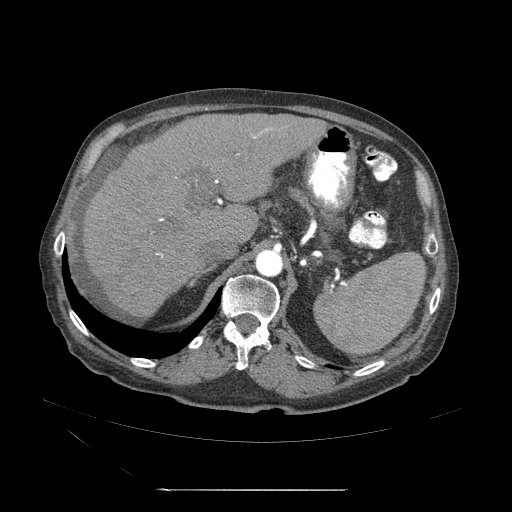
Contrast-enhanced abdominal CT (liver protocol), one axial slice. Slice 32 of 71 in the series (ordered by position). 120 kVp. Soft-tissue window (W 400 / L 40 HU). 2.5 mm slice thickness. 512 × 512 image matrix, field of view 440 × 440 mm. Case-level facts recorded for this patient, not image findings: diagnosis: hepatocellular carcinoma (patient treated with transarterial chemoembolisation; whether this scan precedes or follows treatment is not stated here); TNM stage (as recorded): Stage-II; Child-Pugh class: A; tumour nodularity: multinodular.
Outlined on this slice (semi-automatic segmentation, software-assisted and operator-edited):
- abdominal aorta: box from (x=255, y=247) to (x=284, y=277) px
- liver parenchyma outside the tumour (the mass and vessels are separate outlines, so this box may not span the whole liver): (x=79, y=115)–(x=326, y=323)
- liver vessels: (x=128, y=161)–(x=237, y=290)